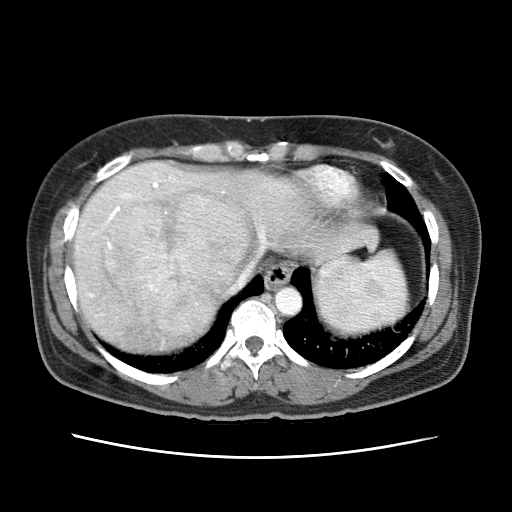
Contrast-enhanced abdominal CT (liver protocol), one axial slice; position 57 of 79 along the scan axis; reconstruction kernel STANDARD; 120 kVp; soft-tissue window (W 400 / L 40 HU); 512 × 512 image matrix, field of view 340 × 340 mm. Case-level facts recorded for this patient, not image findings: diagnosis: hepatocellular carcinoma (patient treated with transarterial chemoembolisation; whether this scan precedes or follows treatment is not stated here); TNM stage (as recorded): Stage-I; Child-Pugh class: A; tumour nodularity: uninodular.
Outlined on this slice (semi-automatically segmented with operator editing):
- abdominal aorta: bounding box [x1, y1, x2, y2] px = [274, 286, 301, 315]
- liver parenchyma outside the tumour (the mass and vessels are separate outlines, so this box may not span the whole liver): [74, 162, 378, 352]
- mass: [106, 189, 249, 337]
- liver vessels: [89, 177, 264, 296]